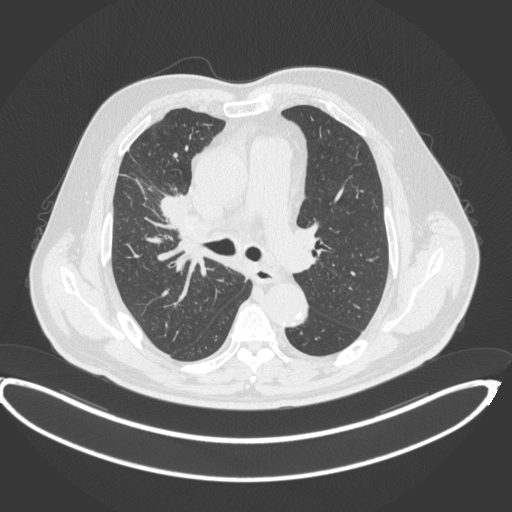
Chest CT, one axial slice; position 259 of 395 along the scan axis; lung window (W 1500 / L -600 HU); 1 mm slice thickness; 512 × 512 image matrix. Male patient, age 62 years. From the clinical record (not read from this slice): clinical TNM (as recorded): T1c N3 M1c.
Structures marked on this image (rectangle marked by the reading radiologist):
- lung tumour (recorded histology: adenocarcinoma): bounding box [x1, y1, x2, y2] px = [153, 188, 194, 222]